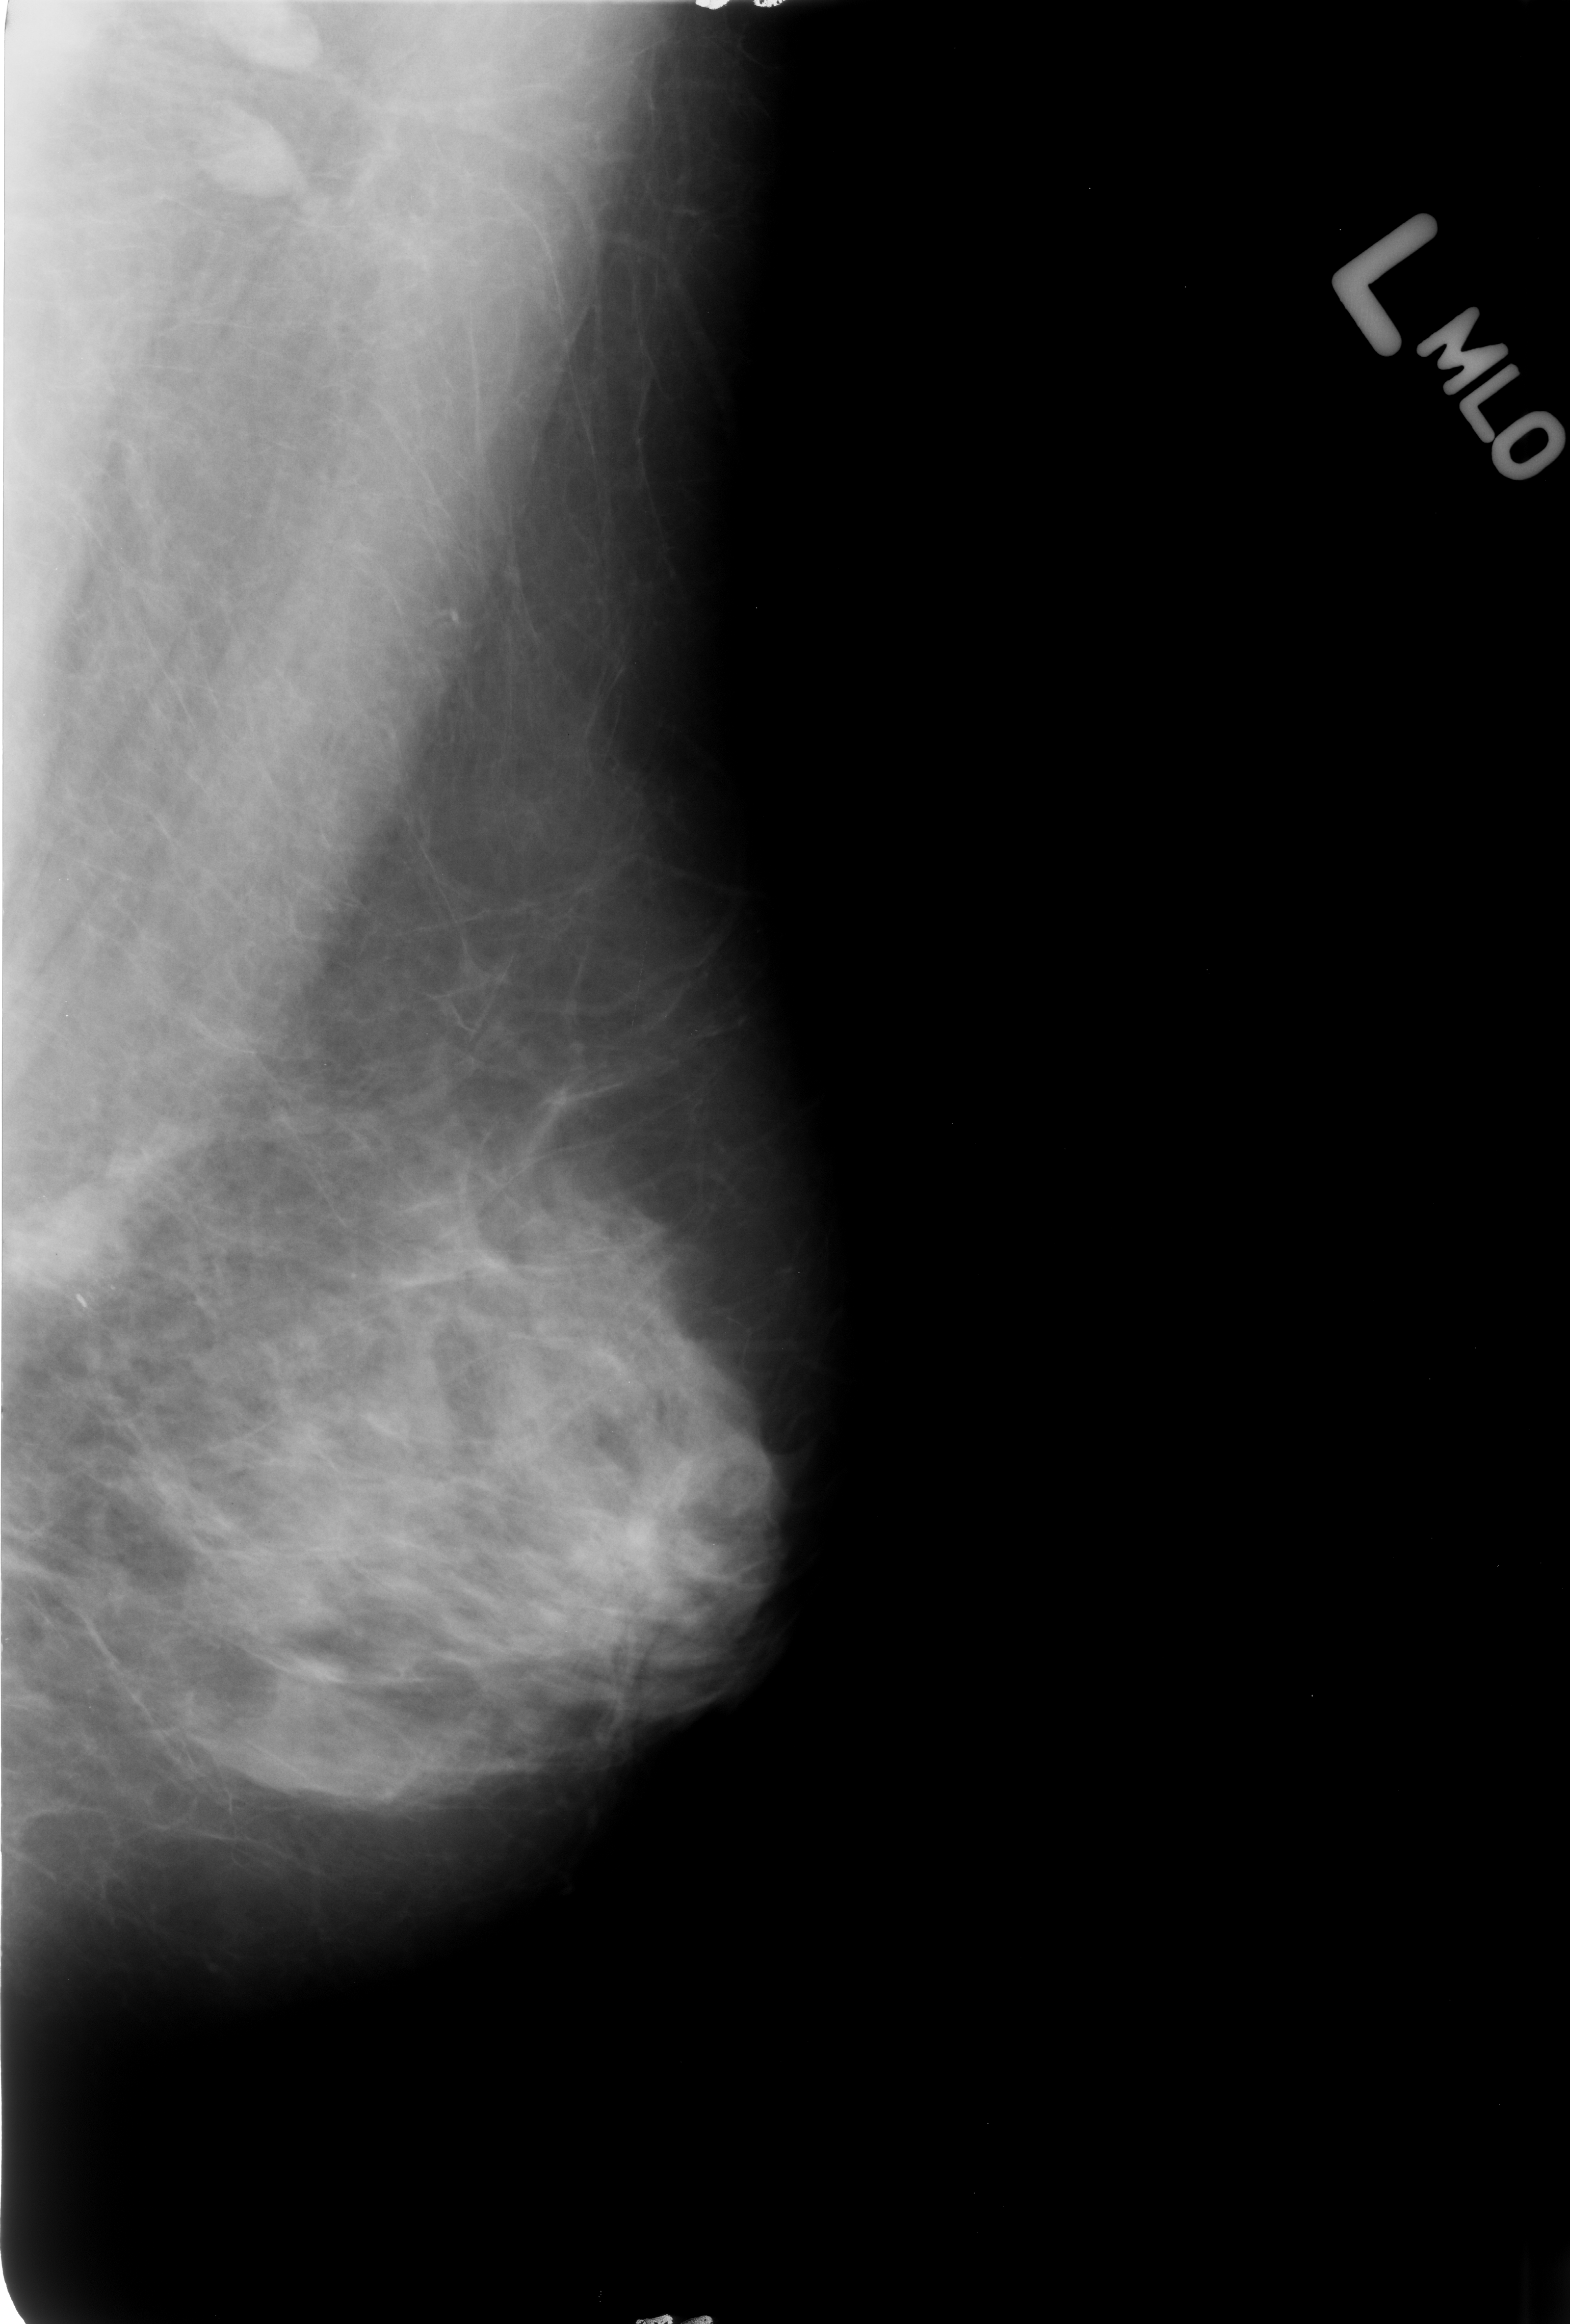
Scanned film-screen mammogram. Left breast. Mediolateral oblique (MLO) view. Breast composition: heterogeneously dense (BI-RADS density category 3 of 4). 1570 × 2324 image matrix.
Expert-marked regions of interest on this film, with their recorded descriptors:
- calcifications, morphology pleomorphic, distribution clustered; BI-RADS assessment category 4; subtlety rating 4 on a 1 (subtle) to 5 (obvious) scale; pathology (as recorded): malignant: box from (x=4, y=1166) to (x=164, y=1342) px